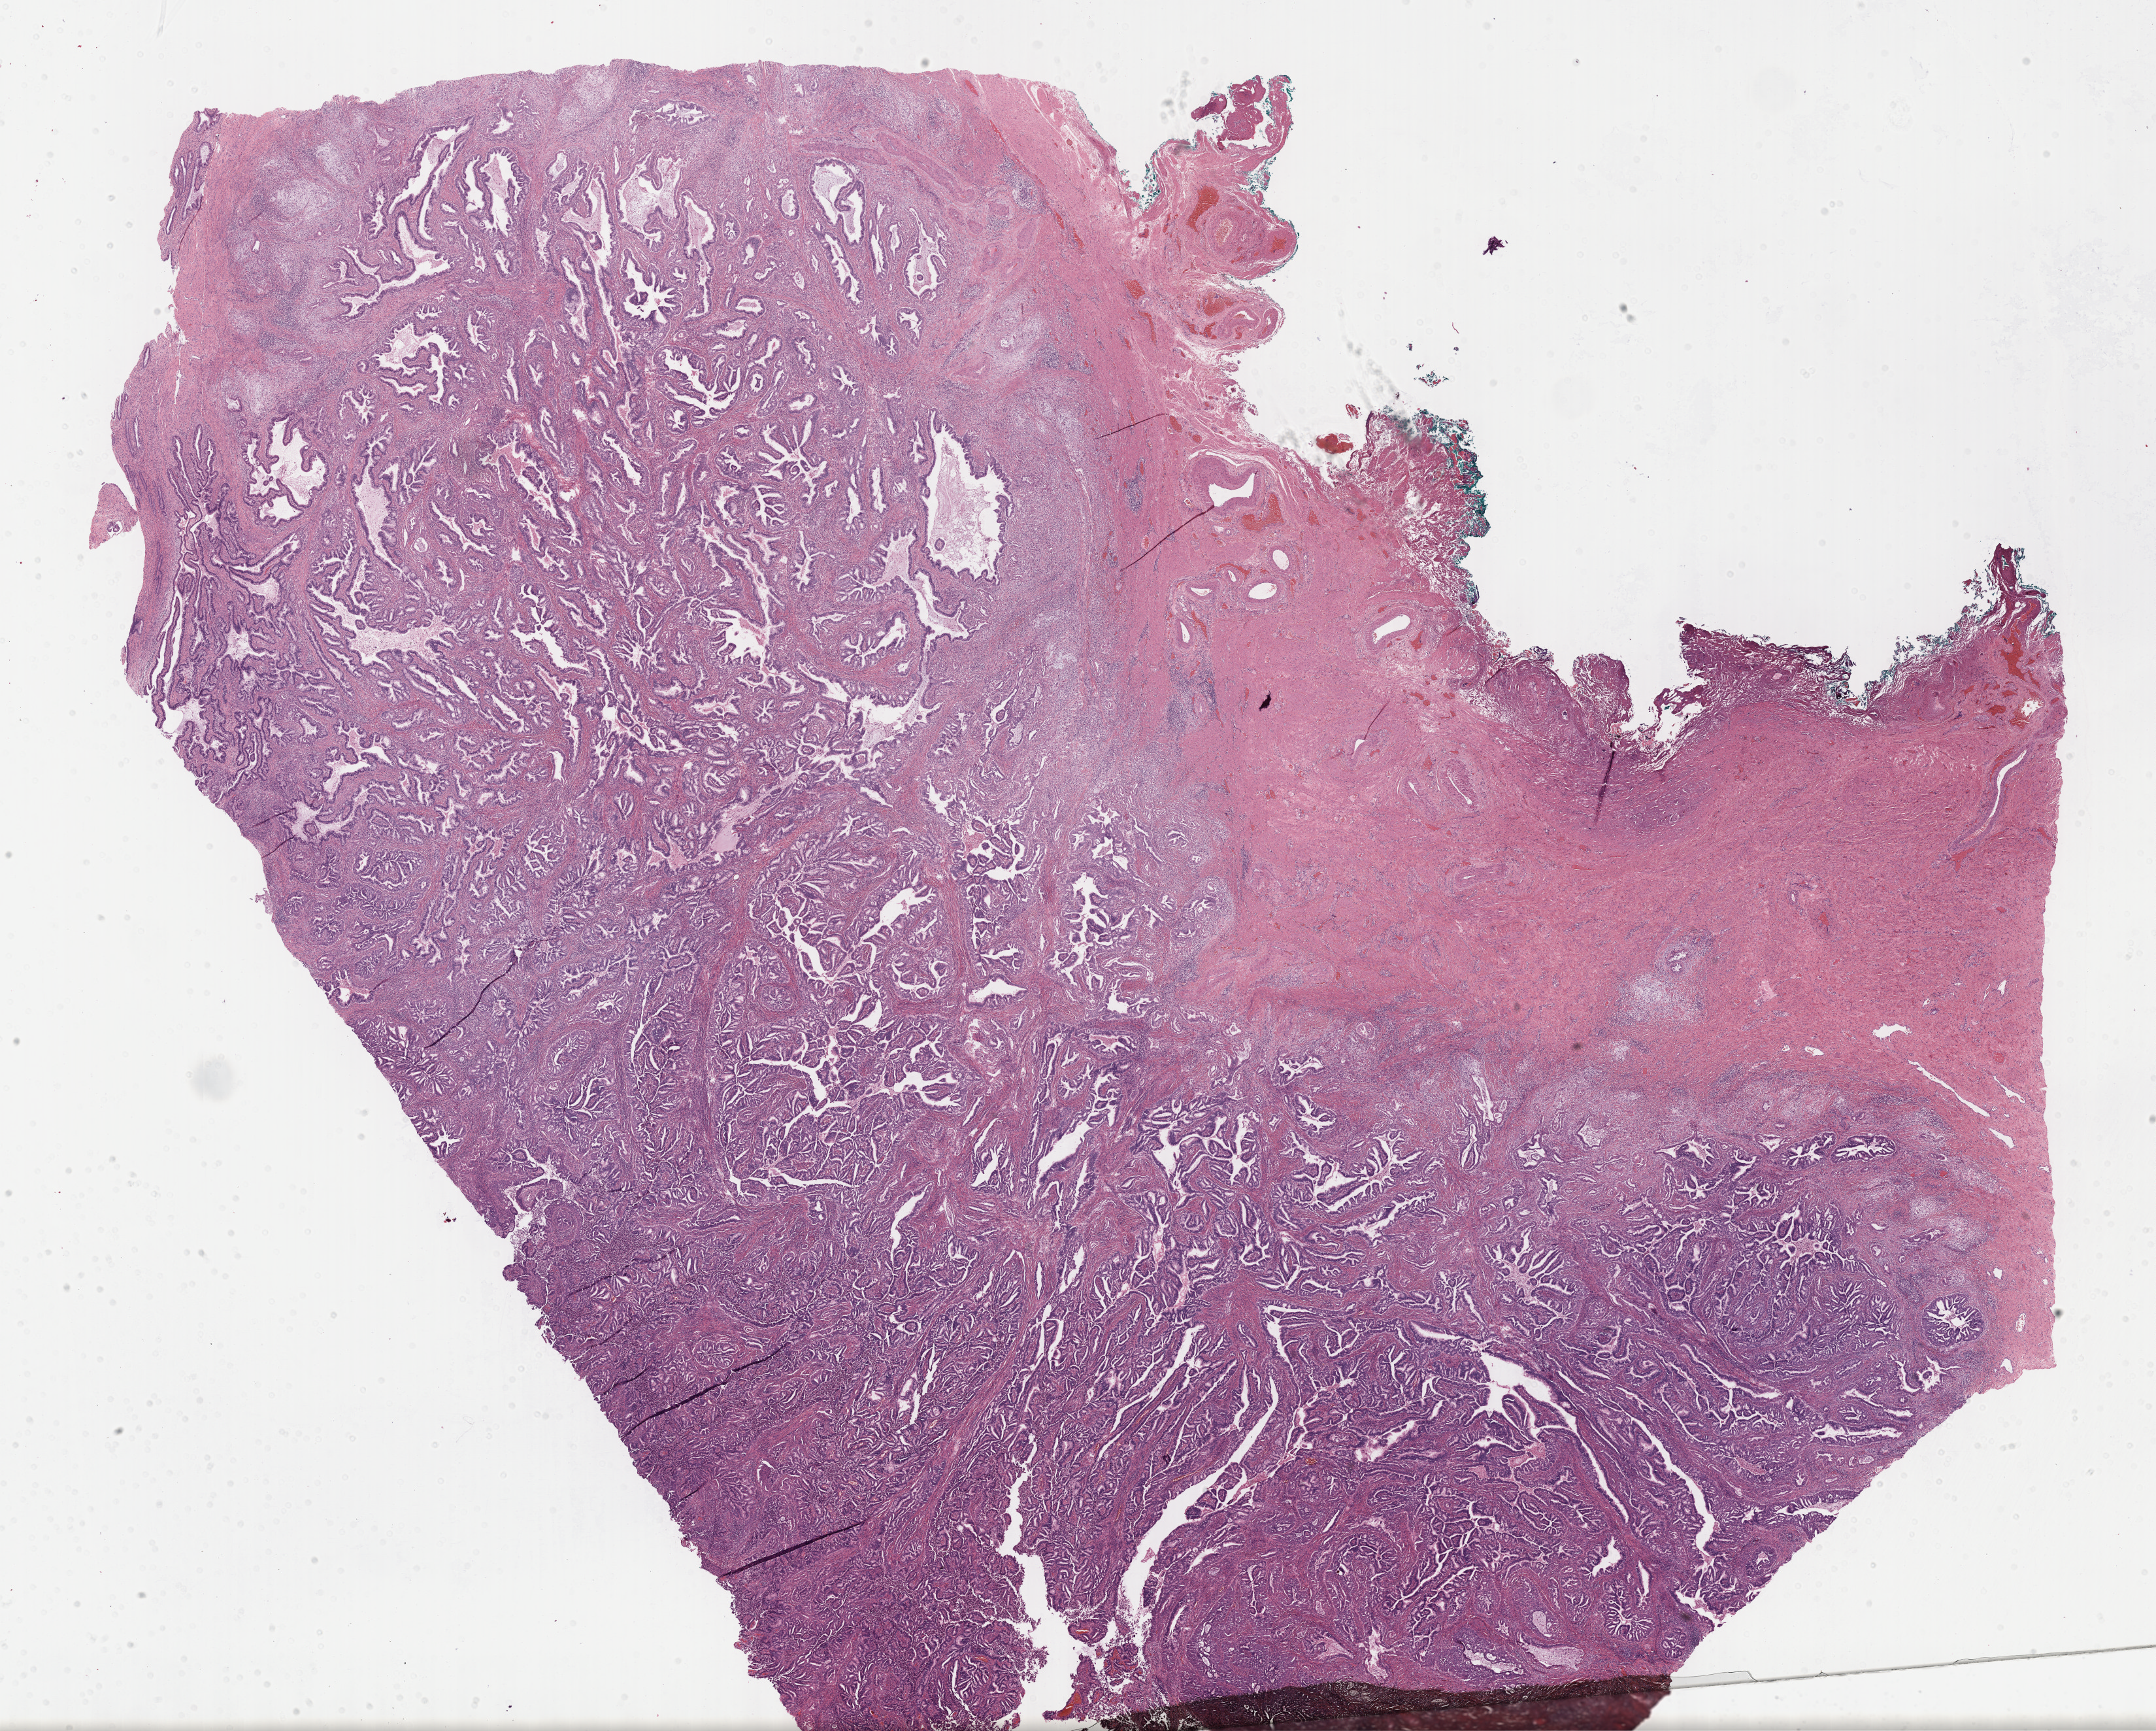
Hematoxylin and eosin (H&E) stained whole-slide image, shown as a low-resolution overview of the whole scanned area (about 26.7 x 21.4 mm, acquisition: 40x scan); formalin-fixed paraffin-embedded (FFPE) diagnostic section; primary tumour sample from the cervix. Patient: female, age at initial diagnosis 32 years. Histologic grade: G2 (moderately differentiated).
FIGO stage: IB. Lymph nodes positive (case pathology): 0 of 22 examined. Diagnosis: Mucinous adenocarcinoma, endocervical type (cervix uteri).